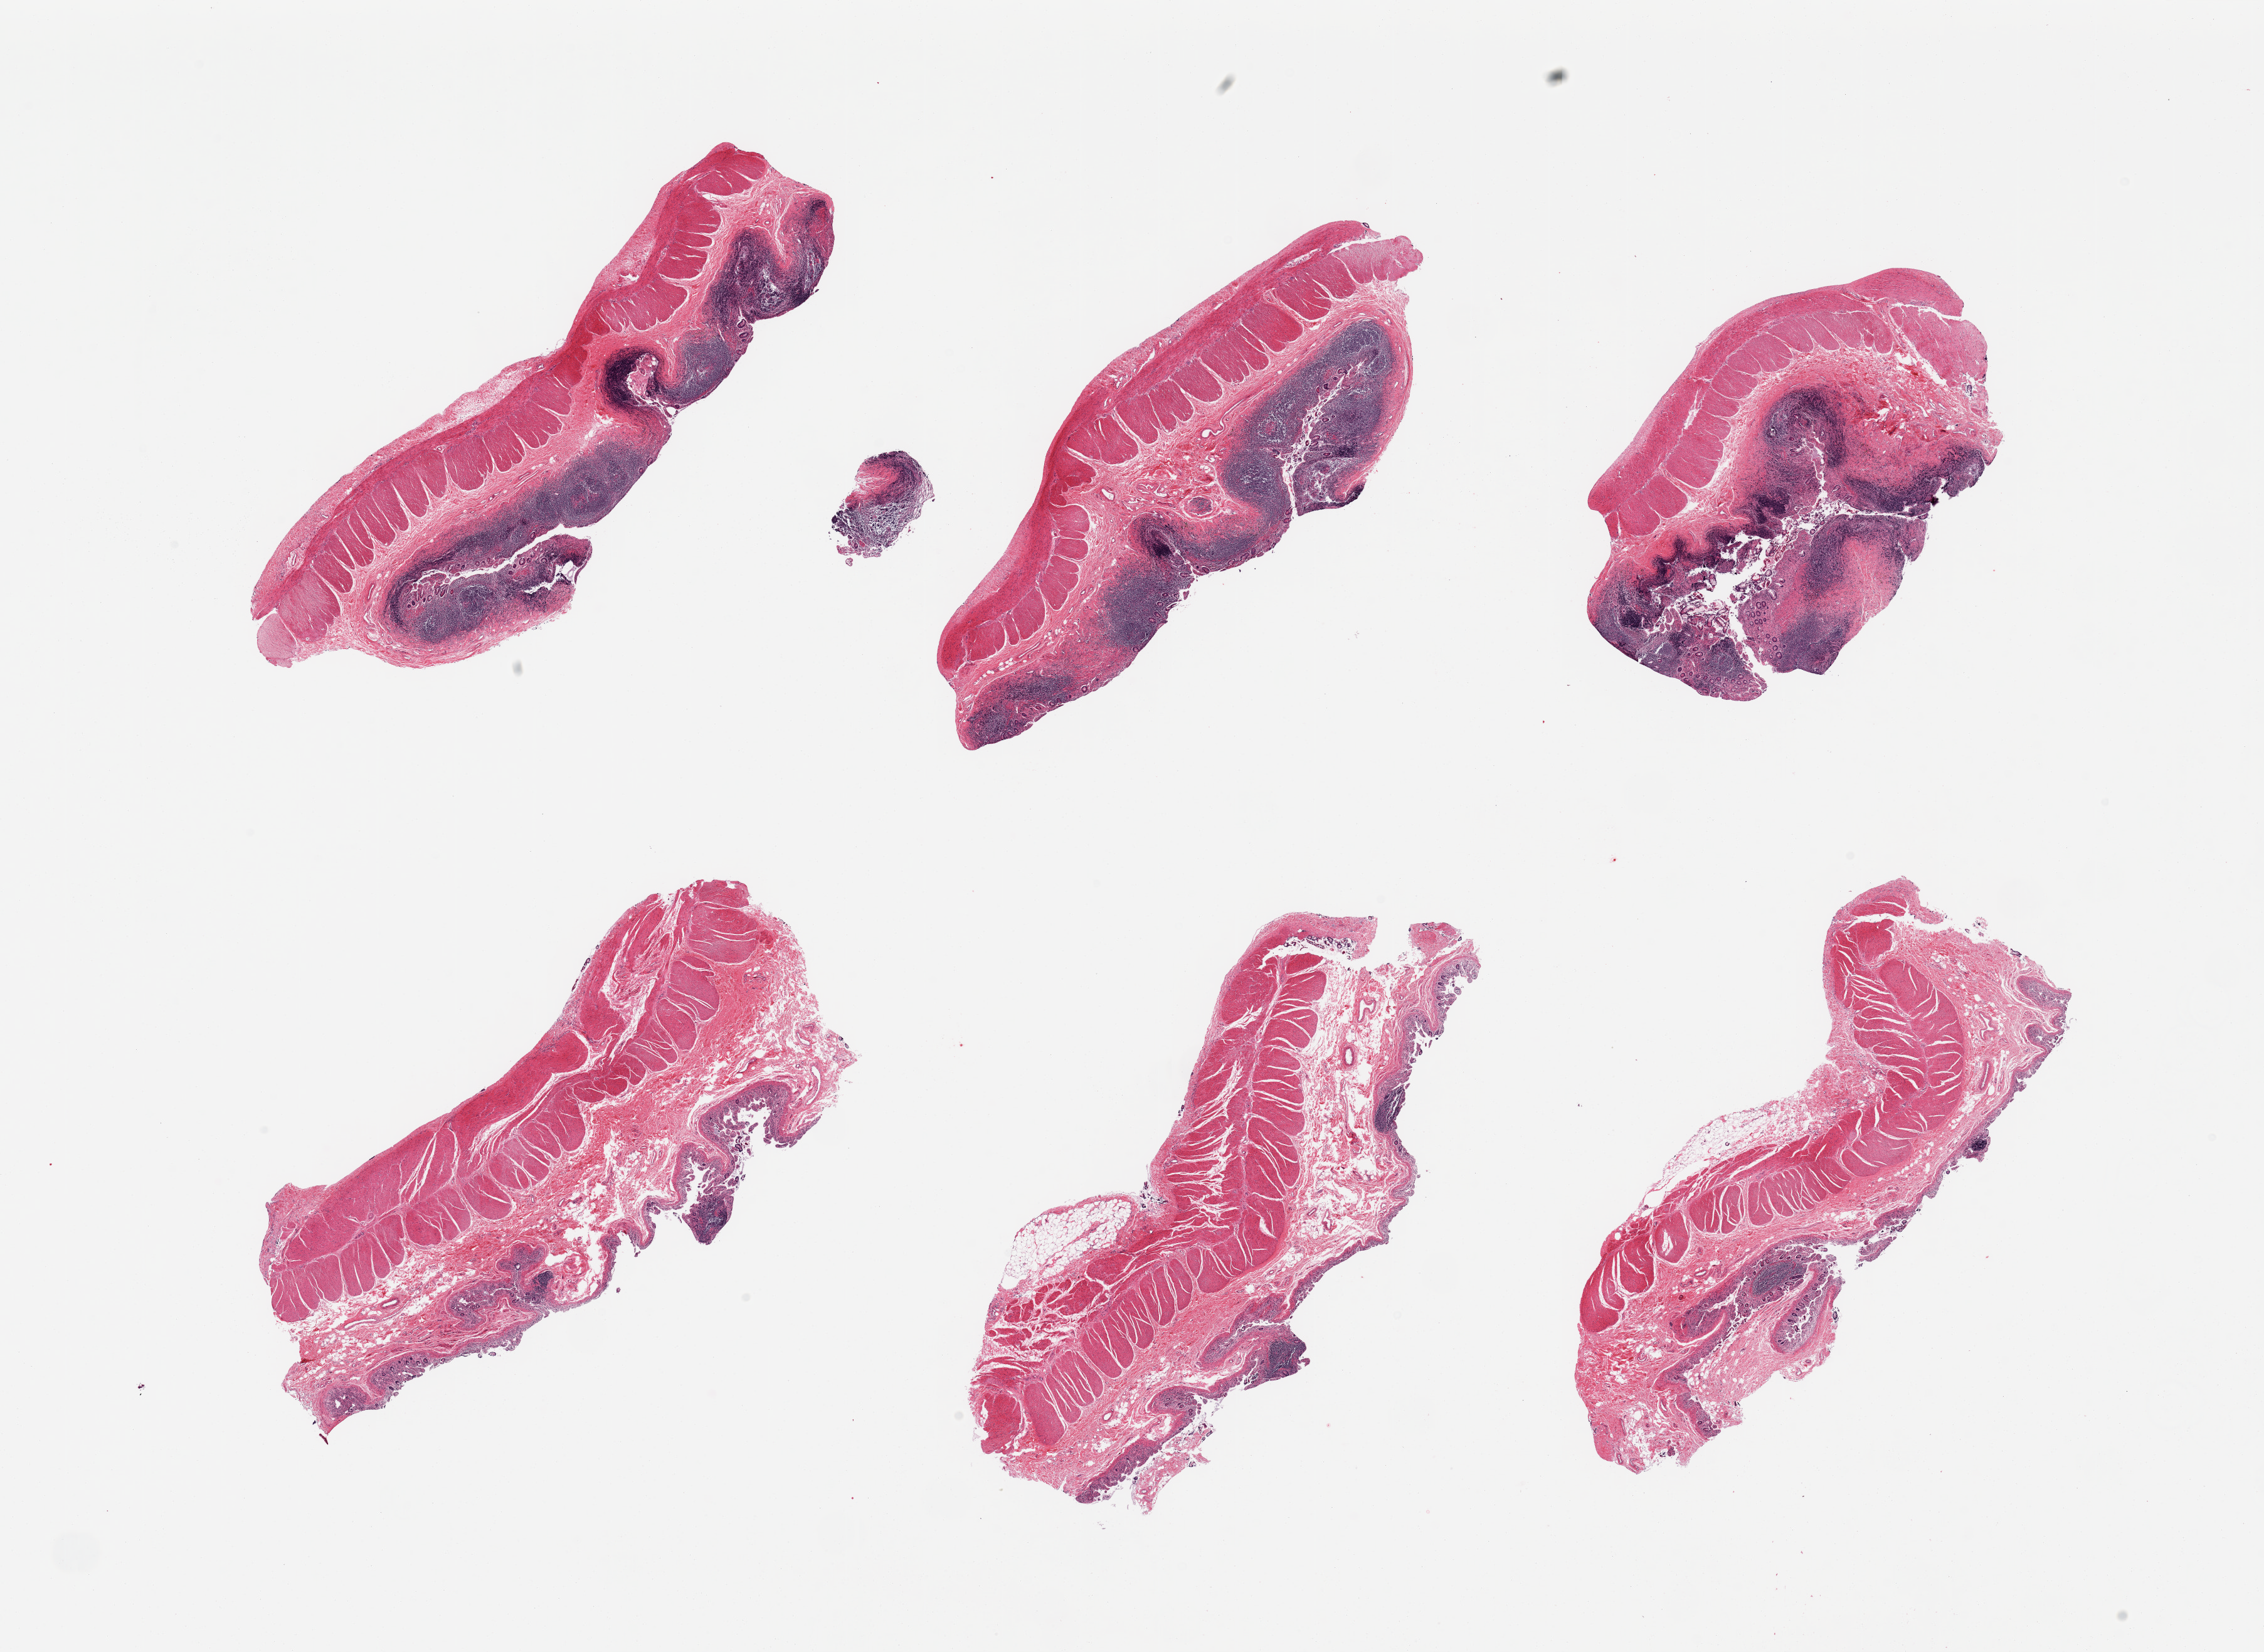
Whole-slide image, haematoxylin and eosin stain — low-resolution overview of the scanned area, about 28.5 x 20.8 mm; PAXgene-fixed, paraffin-embedded tissue; sampled site (target tissue): ileum; donor tissue sample. Female donor.
Reviewer comment on this tissue sample: 6 pieces; abundant lymphoid tissue on 3 pieces; muscularis present on all.